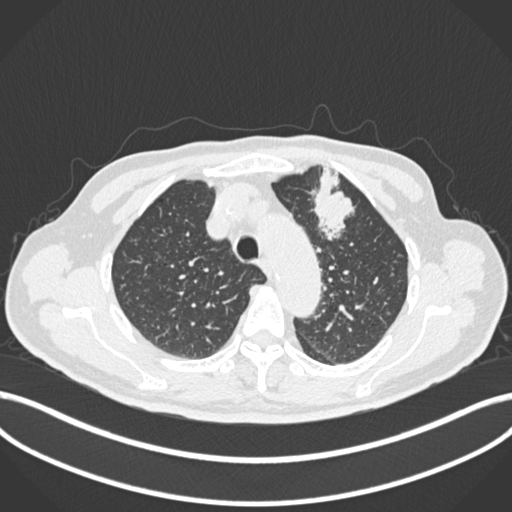
Chest CT, one axial slice. Position 198 of 261 along the scan axis. Reconstruction kernel B30f. Lung window (W 1500 / L -600 HU). 1 mm slice thickness. 512 × 512 image matrix, field of view 400 × 400 mm. Patient: male, 74 years. From the clinical record (not read from this slice): clinical TNM (as recorded): T2b N0 M1c.
Outlined on this slice (rectangle marked by the reading radiologist):
- lung tumour (recorded histology: adenocarcinoma): bounding box [x1, y1, x2, y2] px = [311, 164, 363, 245]